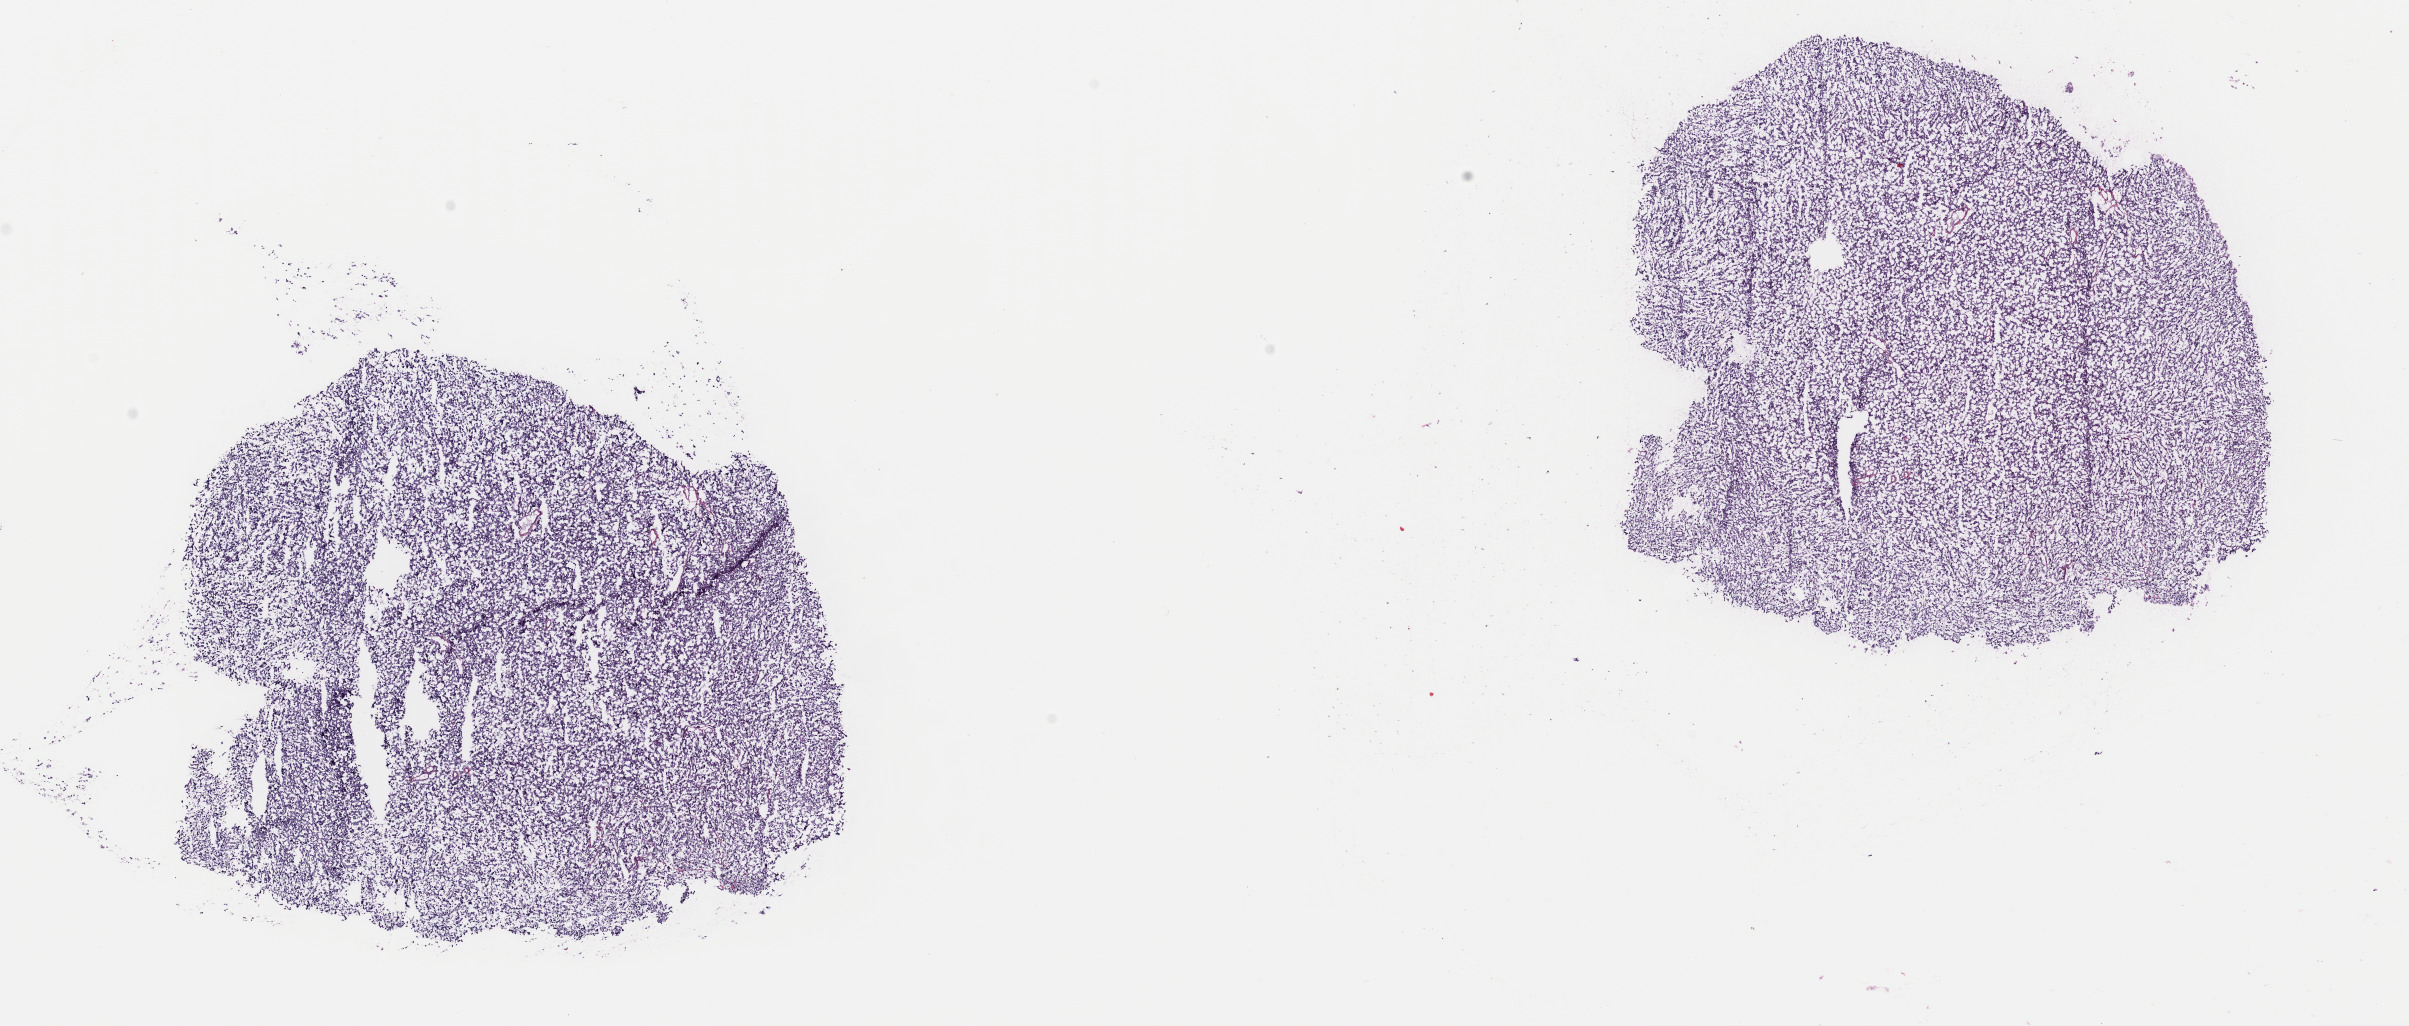
Digitized Hematoxylin and eosin (H&E) stained tissue section (whole slide) — a low-resolution overview of the entire scanned area, about 19.0 x 8.1 mm (acquisition: 40x scan), frozen section from the top of the tissue portion, adrenal gland, primary tumour sample. Male, age 40 years at initial diagnosis. Slide review estimates, as recorded: tumour cells 100%, tumour nuclei 80%, normal cells 0%, stromal cells 0%, necrosis 0%. Infiltration values recorded for this section: lymphocyte infiltration 1%, monocyte infiltration 0%, neutrophil infiltration 0%.
* histologic diagnosis: Pheochromocytoma, NOS